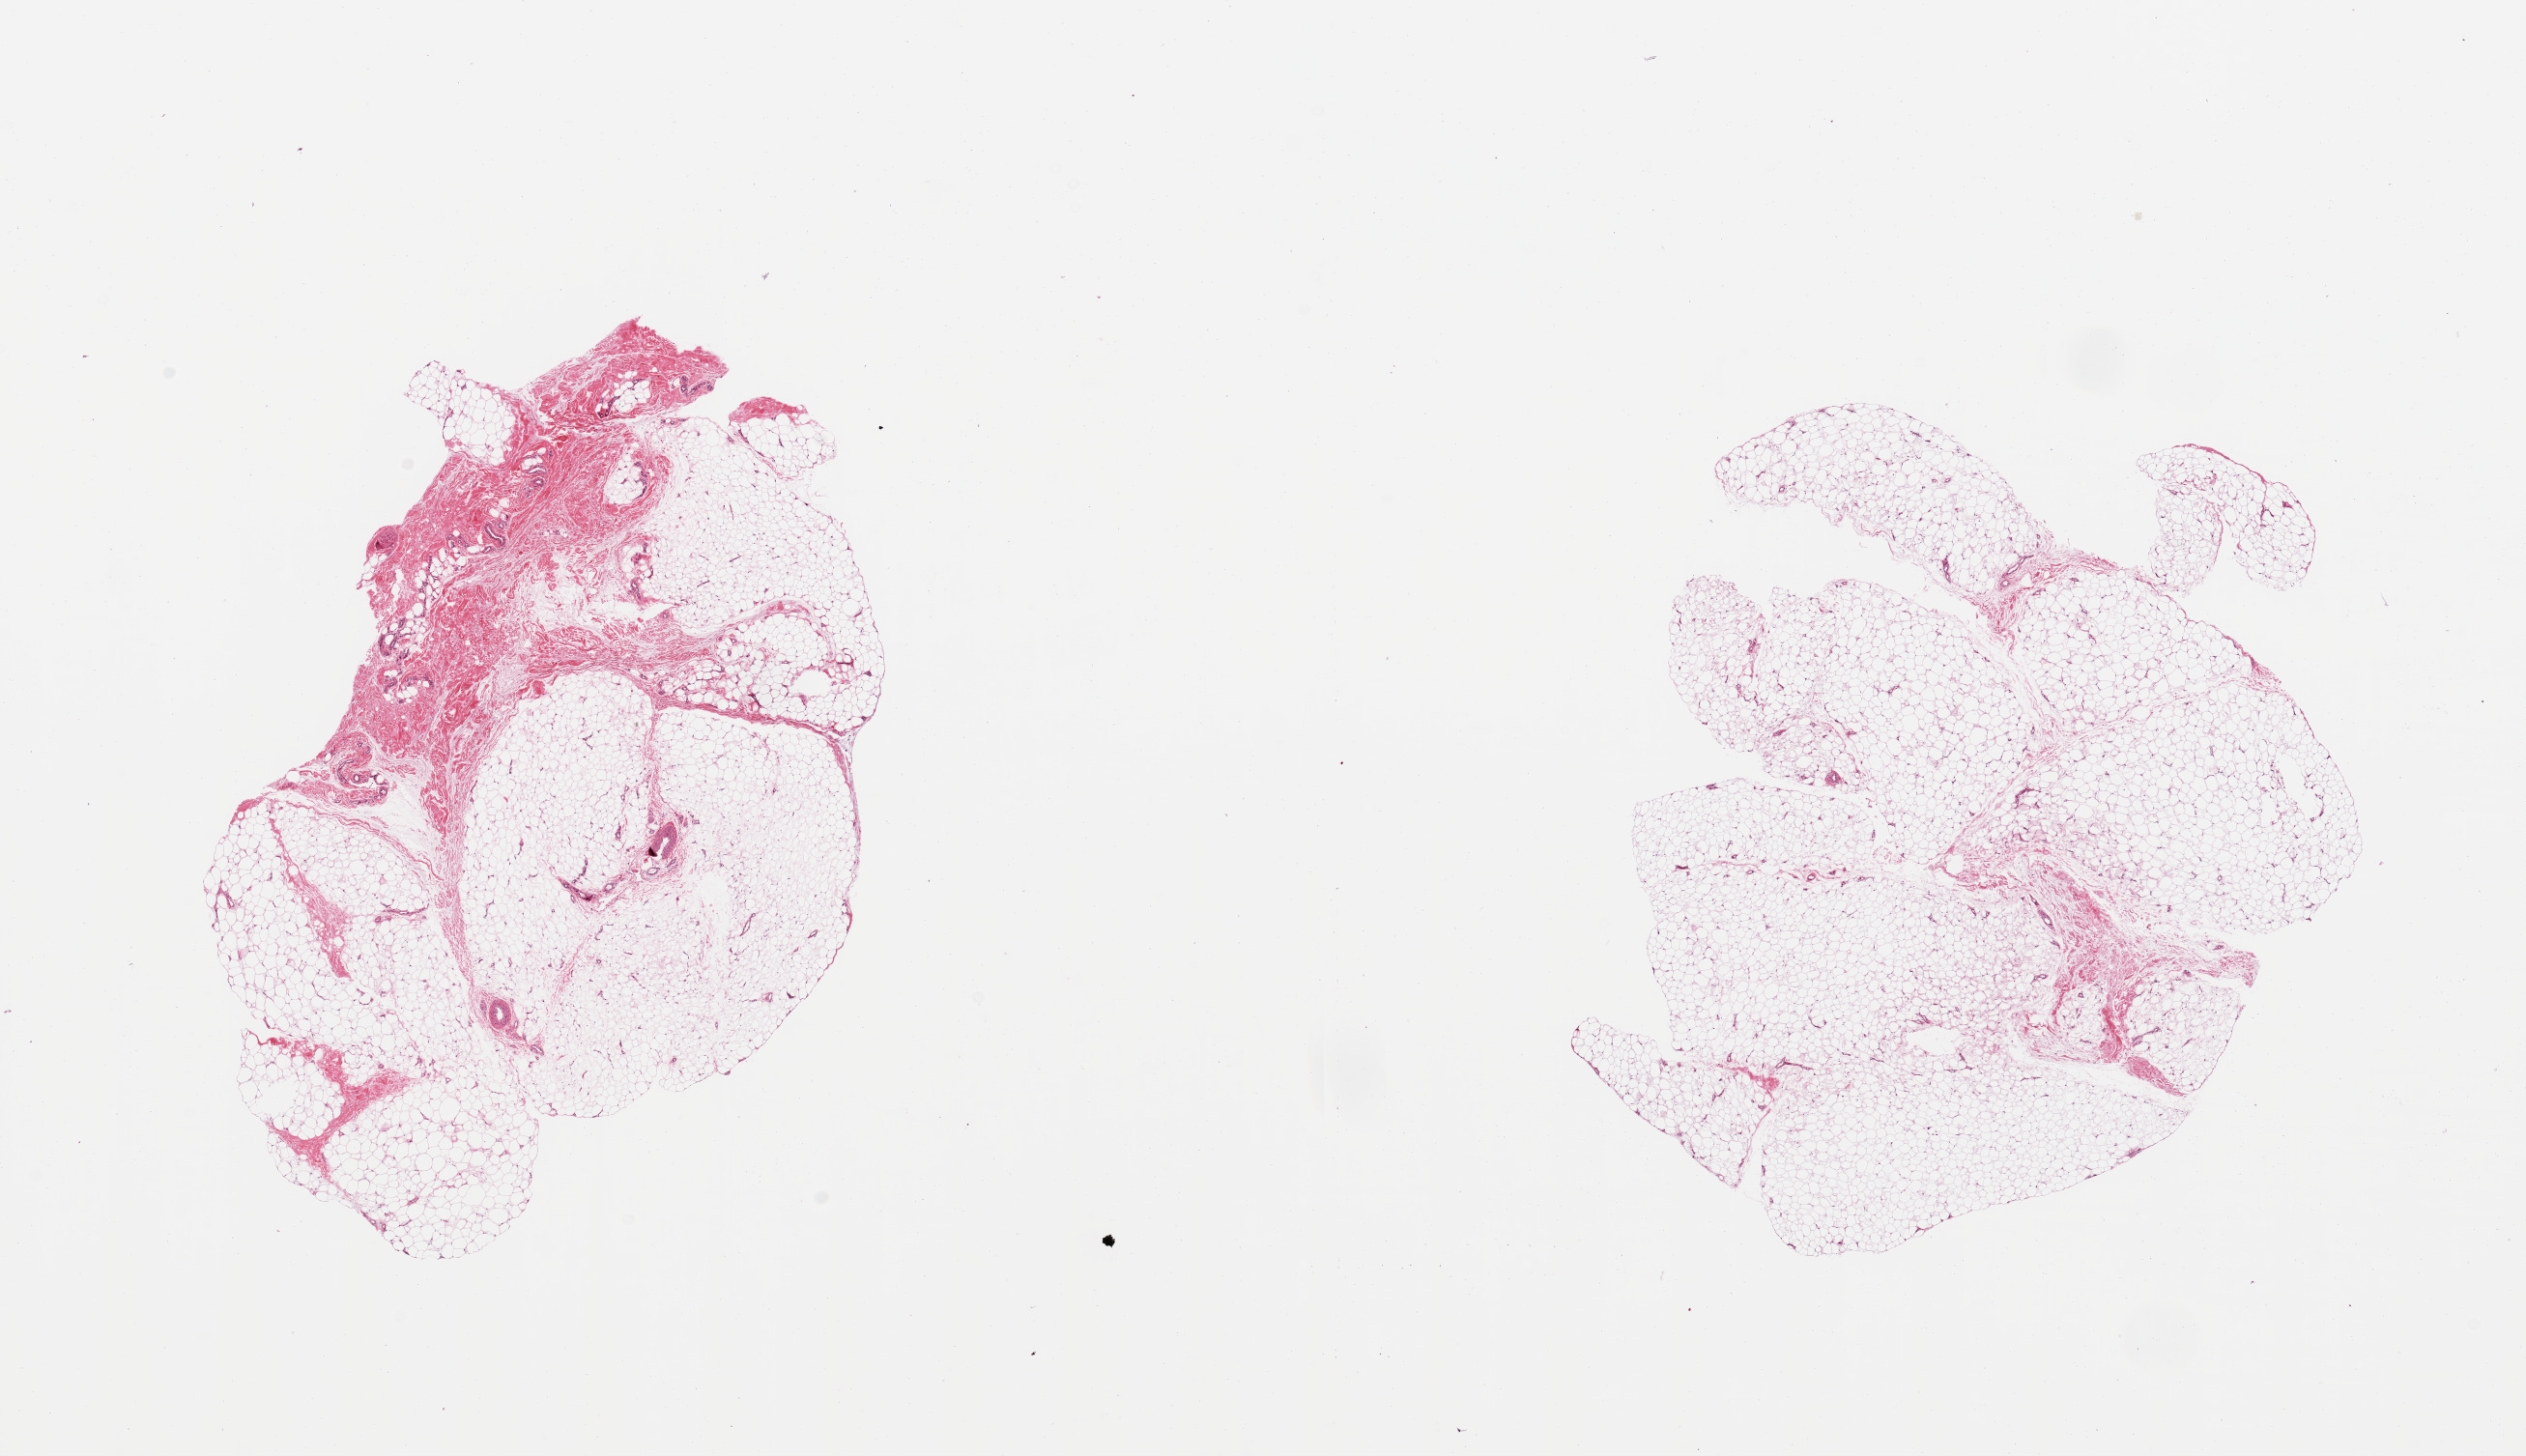
H&E whole-slide image, whole scanned area (about 20.7 x 11.9 mm, acquisition: 20x scan) shown as a low-resolution overview; PAXgene-fixed, paraffin-embedded tissue; target tissue: adipose tissue; tissue donor sample. Male donor.
Reviewer comment on this tissue sample: 2 pieces; 1 contains 25% fibrous tissue.